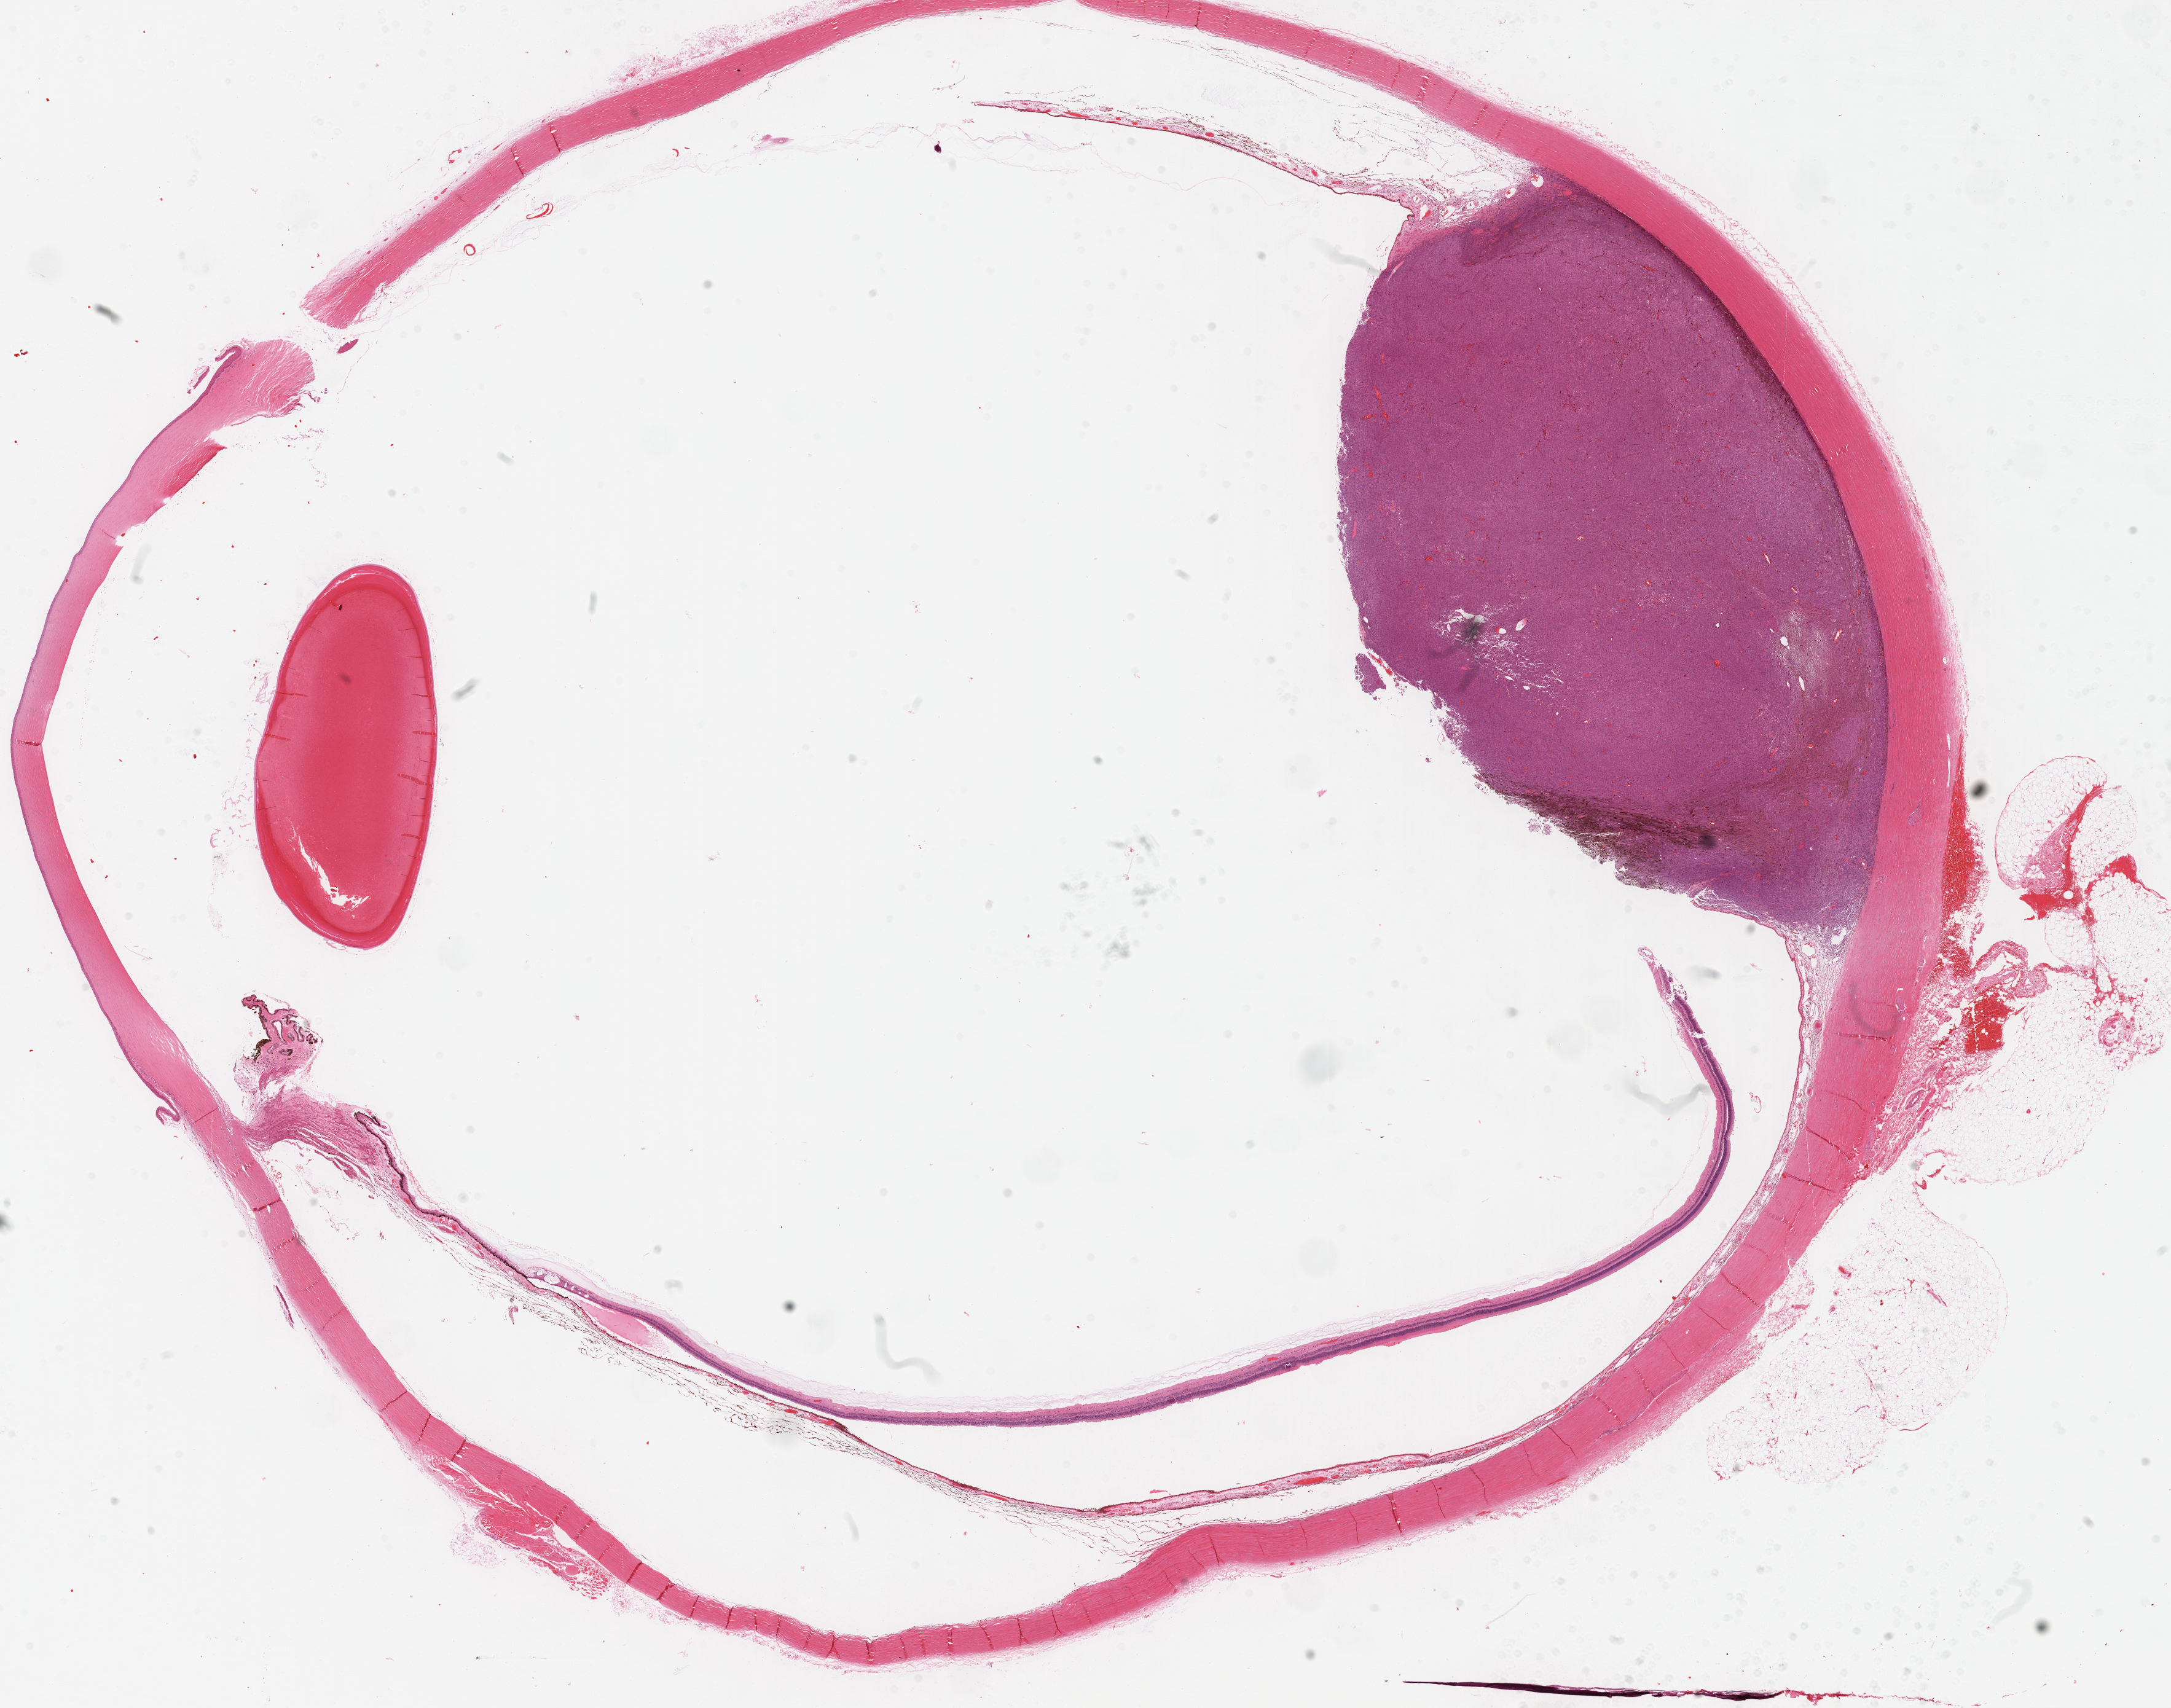
Whole-slide histology image, H&E — whole scanned area (about 28.5 x 22.4 mm) shown as a low-resolution overview, formalin-fixed paraffin-embedded (FFPE) diagnostic section, uvea, primary tumour sample. Male, age 64 years at initial diagnosis.
Laterality: right. AJCC pathologic stage: IIA (7th edition). Pathologic diagnosis: Mixed epithelioid and spindle cell melanoma (choroid).